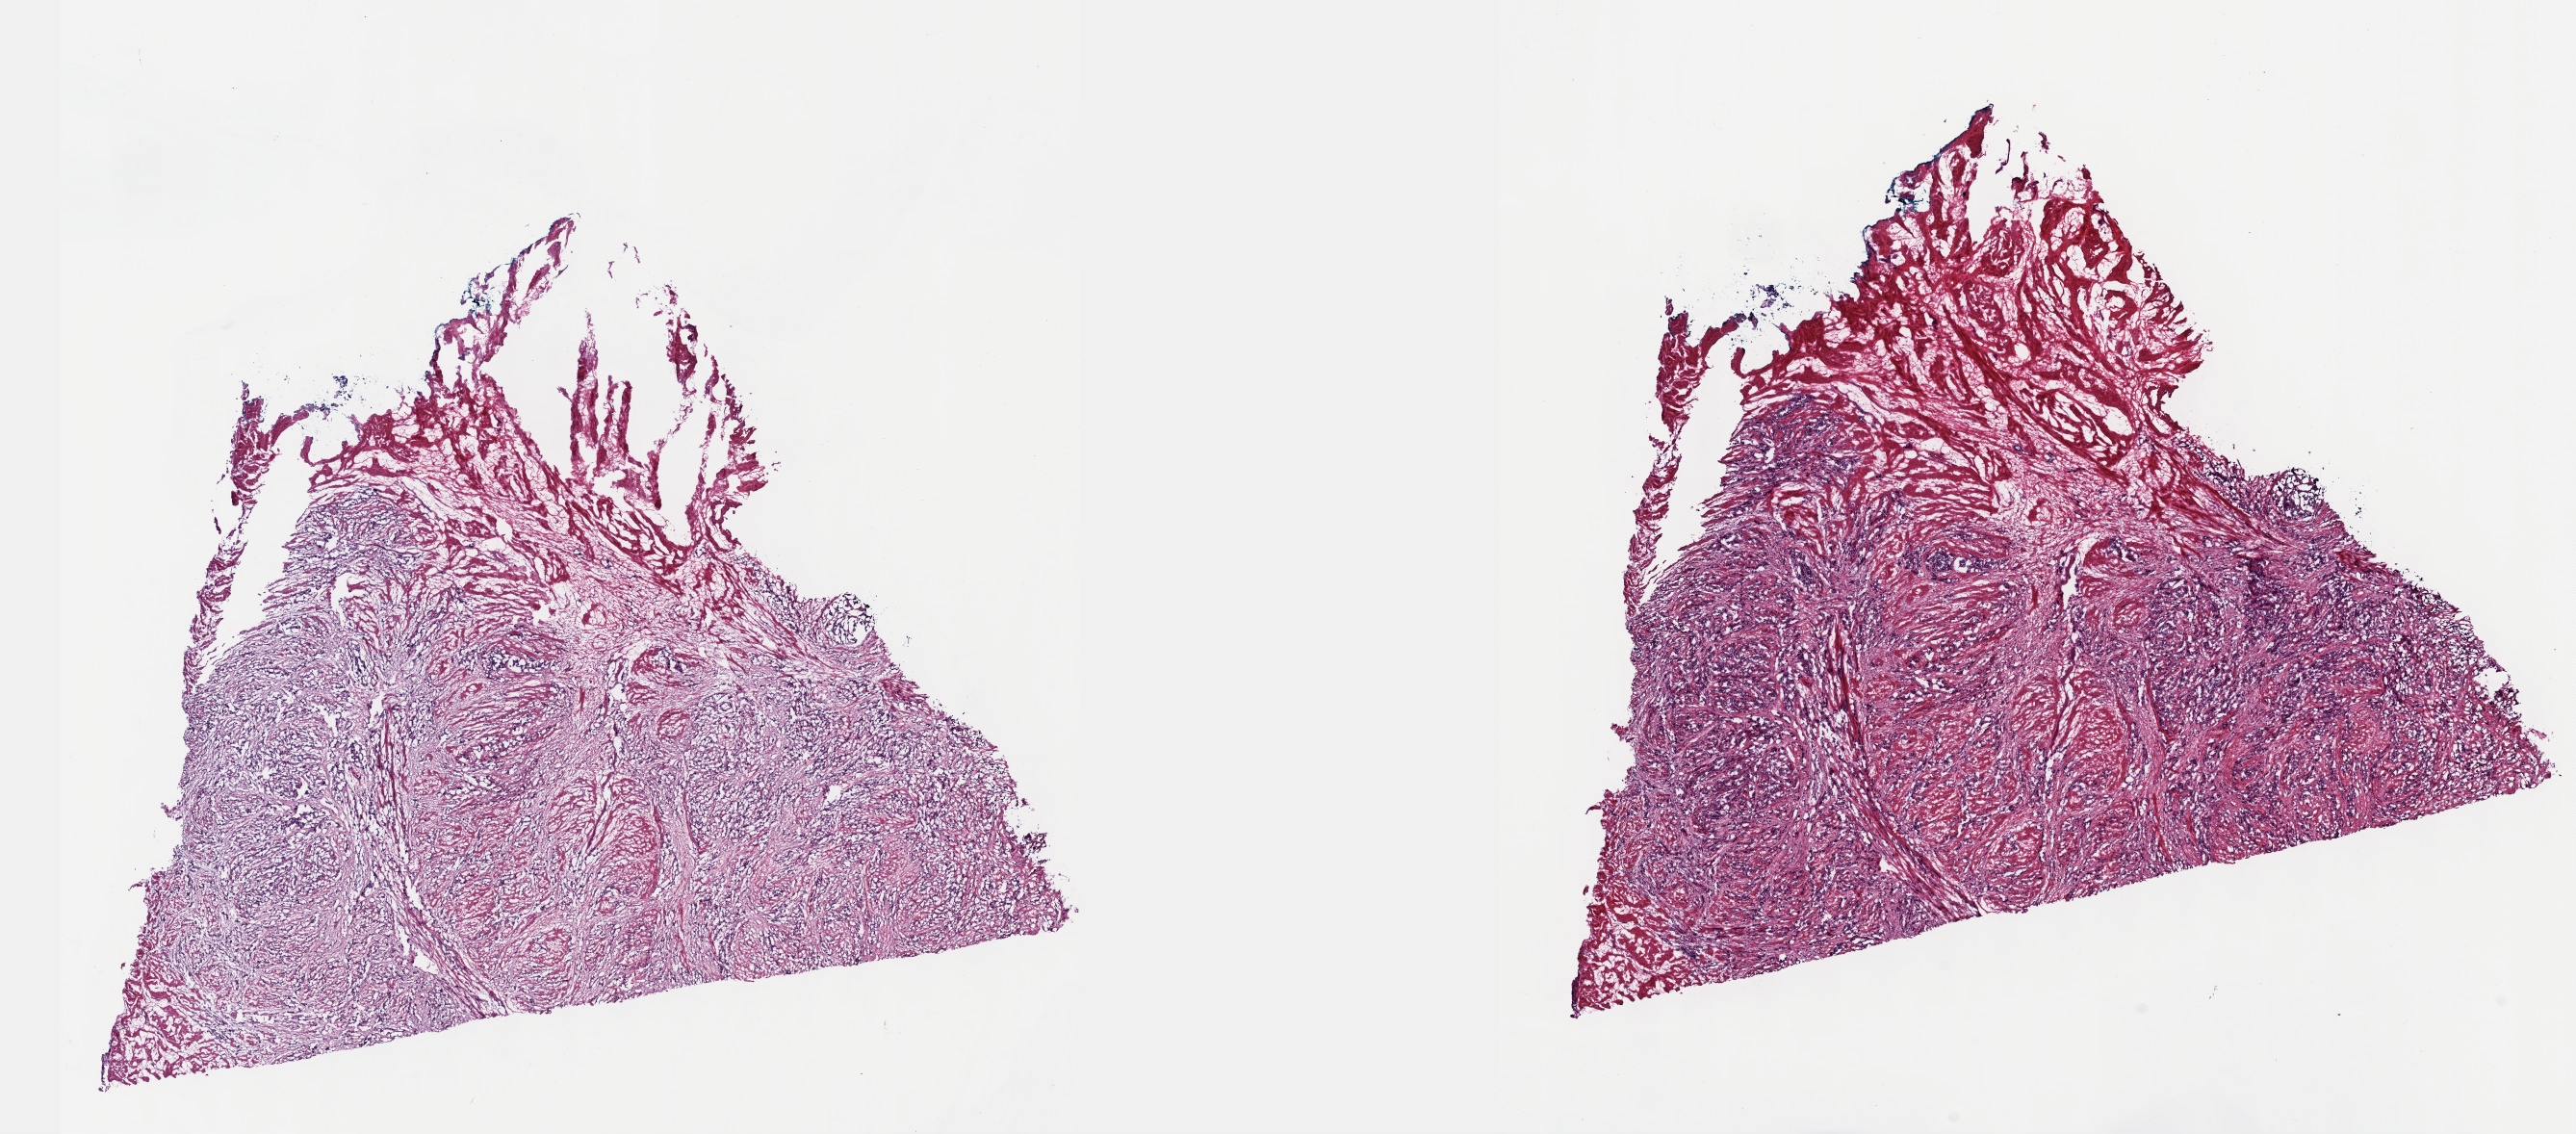
Whole-slide histology image, H&E — low-resolution overview of the scanned area, about 21.6 x 9.5 mm (slide scanned at 40x). Frozen section from the top of the tissue portion. Sample: primary tumour, prostate. Male patient; age at initial diagnosis 60 years. Pathologist review of this section (percent, as recorded): tumour cells 75%, tumour nuclei 75%.
Histologic diagnosis: Adenocarcinoma, NOS (prostate gland).